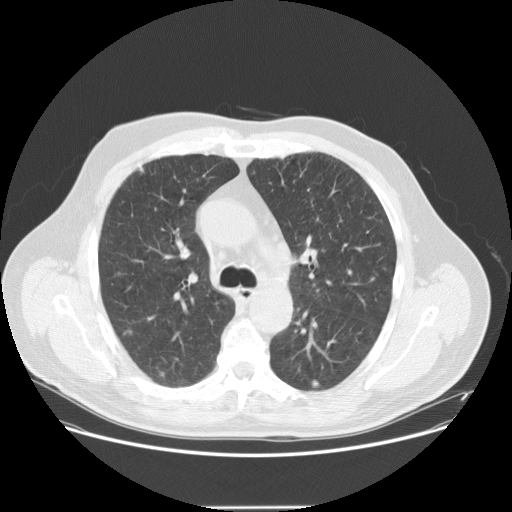
Low-dose screening chest CT, one axial slice. Position 97 of 143 along the scan axis. Reconstruction kernel STANDARD. 120 kVp. Lung window (W 1500 / L -600 HU). 2.5 mm slice thickness. 512 × 512 image matrix, field of view 400 × 400 mm.
Annotated regions visible in this slice (expert manual segmentation):
- lesion 2 (tumor): box from (x=312, y=380) to (x=319, y=387) px
- lesion 6 (tumor, lower lobe of right lung): (x=160, y=372)–(x=164, y=377)